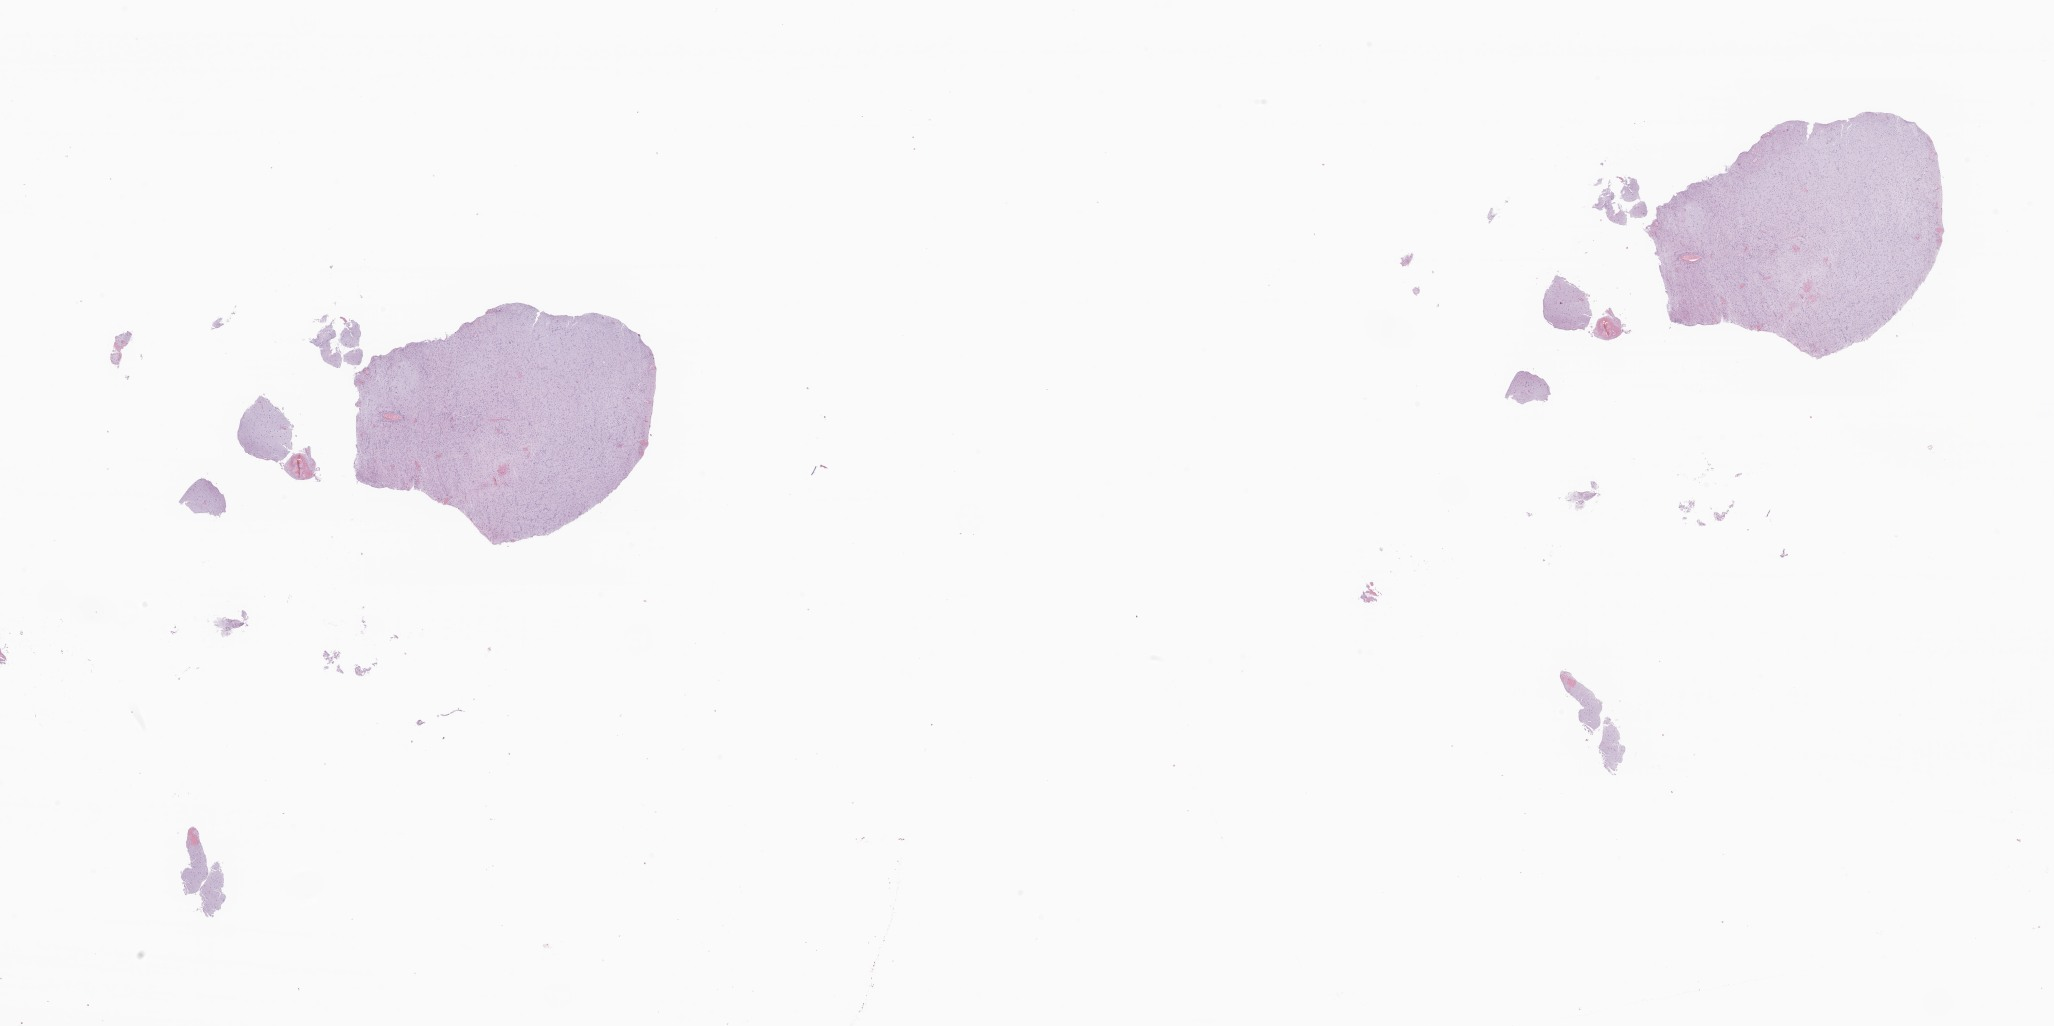
Whole-slide image, H&E stain of tumor tissue from the brain — whole scanned area (about 34.6 x 17.3 mm) shown as a low-resolution overview. FFPE section. Patient female; age 190 months (15 years 10 months).
Recorded diagnosis: Glioma, malignant.